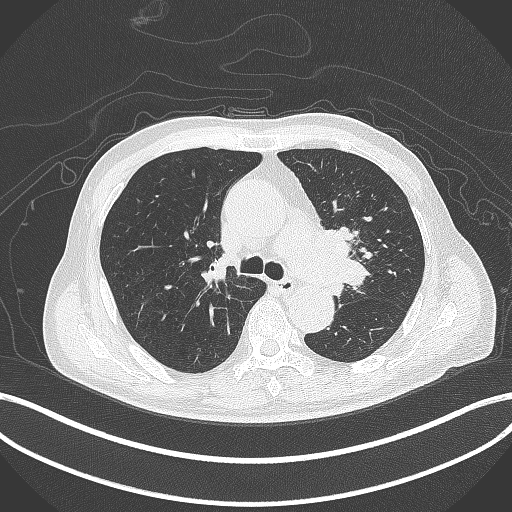
Chest CT, one axial slice; slice 284 of 417 in the series (ordered by position); reconstruction kernel B70f; lung window (W 1500 / L -600 HU); 512 × 512 image matrix, field of view 400 × 400 mm. Patient: male, 77 years. Case-level facts recorded for this patient, not image findings: clinical TNM (as recorded): T3 N1 M0.
Outlined on this slice (bounding box drawn by a radiologist):
- lung tumour (recorded histology: adenocarcinoma): bounding box (x1, y1, x2, y2) in pixels: (322, 222, 372, 295)